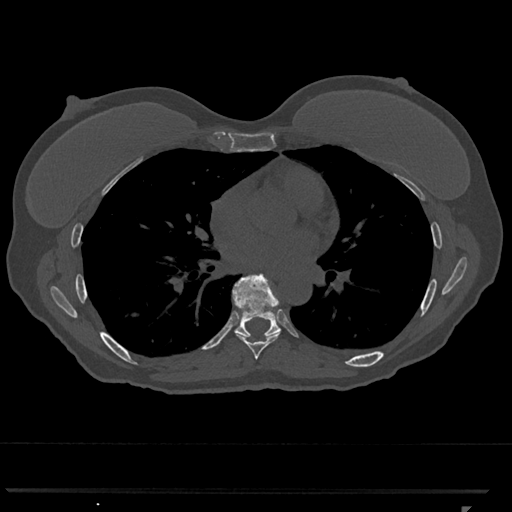
CT including the spine, one axial slice. Slice 692 of 793 in the series (ordered by position). Reconstruction kernel Br40s/3. Bone window (W 1800 / L 400 HU). 512 × 512 image matrix, field of view 380 × 380 mm. Patient: female, 62 years. From the clinical record (not read from this slice): primary cancer: renal.
Structures marked on this image (semi-automatically segmented with operator editing):
- T7 vertebra: bounding box [x1, y1, x2, y2] px = [234, 331, 281, 359]
- T8 vertebra: [233, 273, 281, 337]